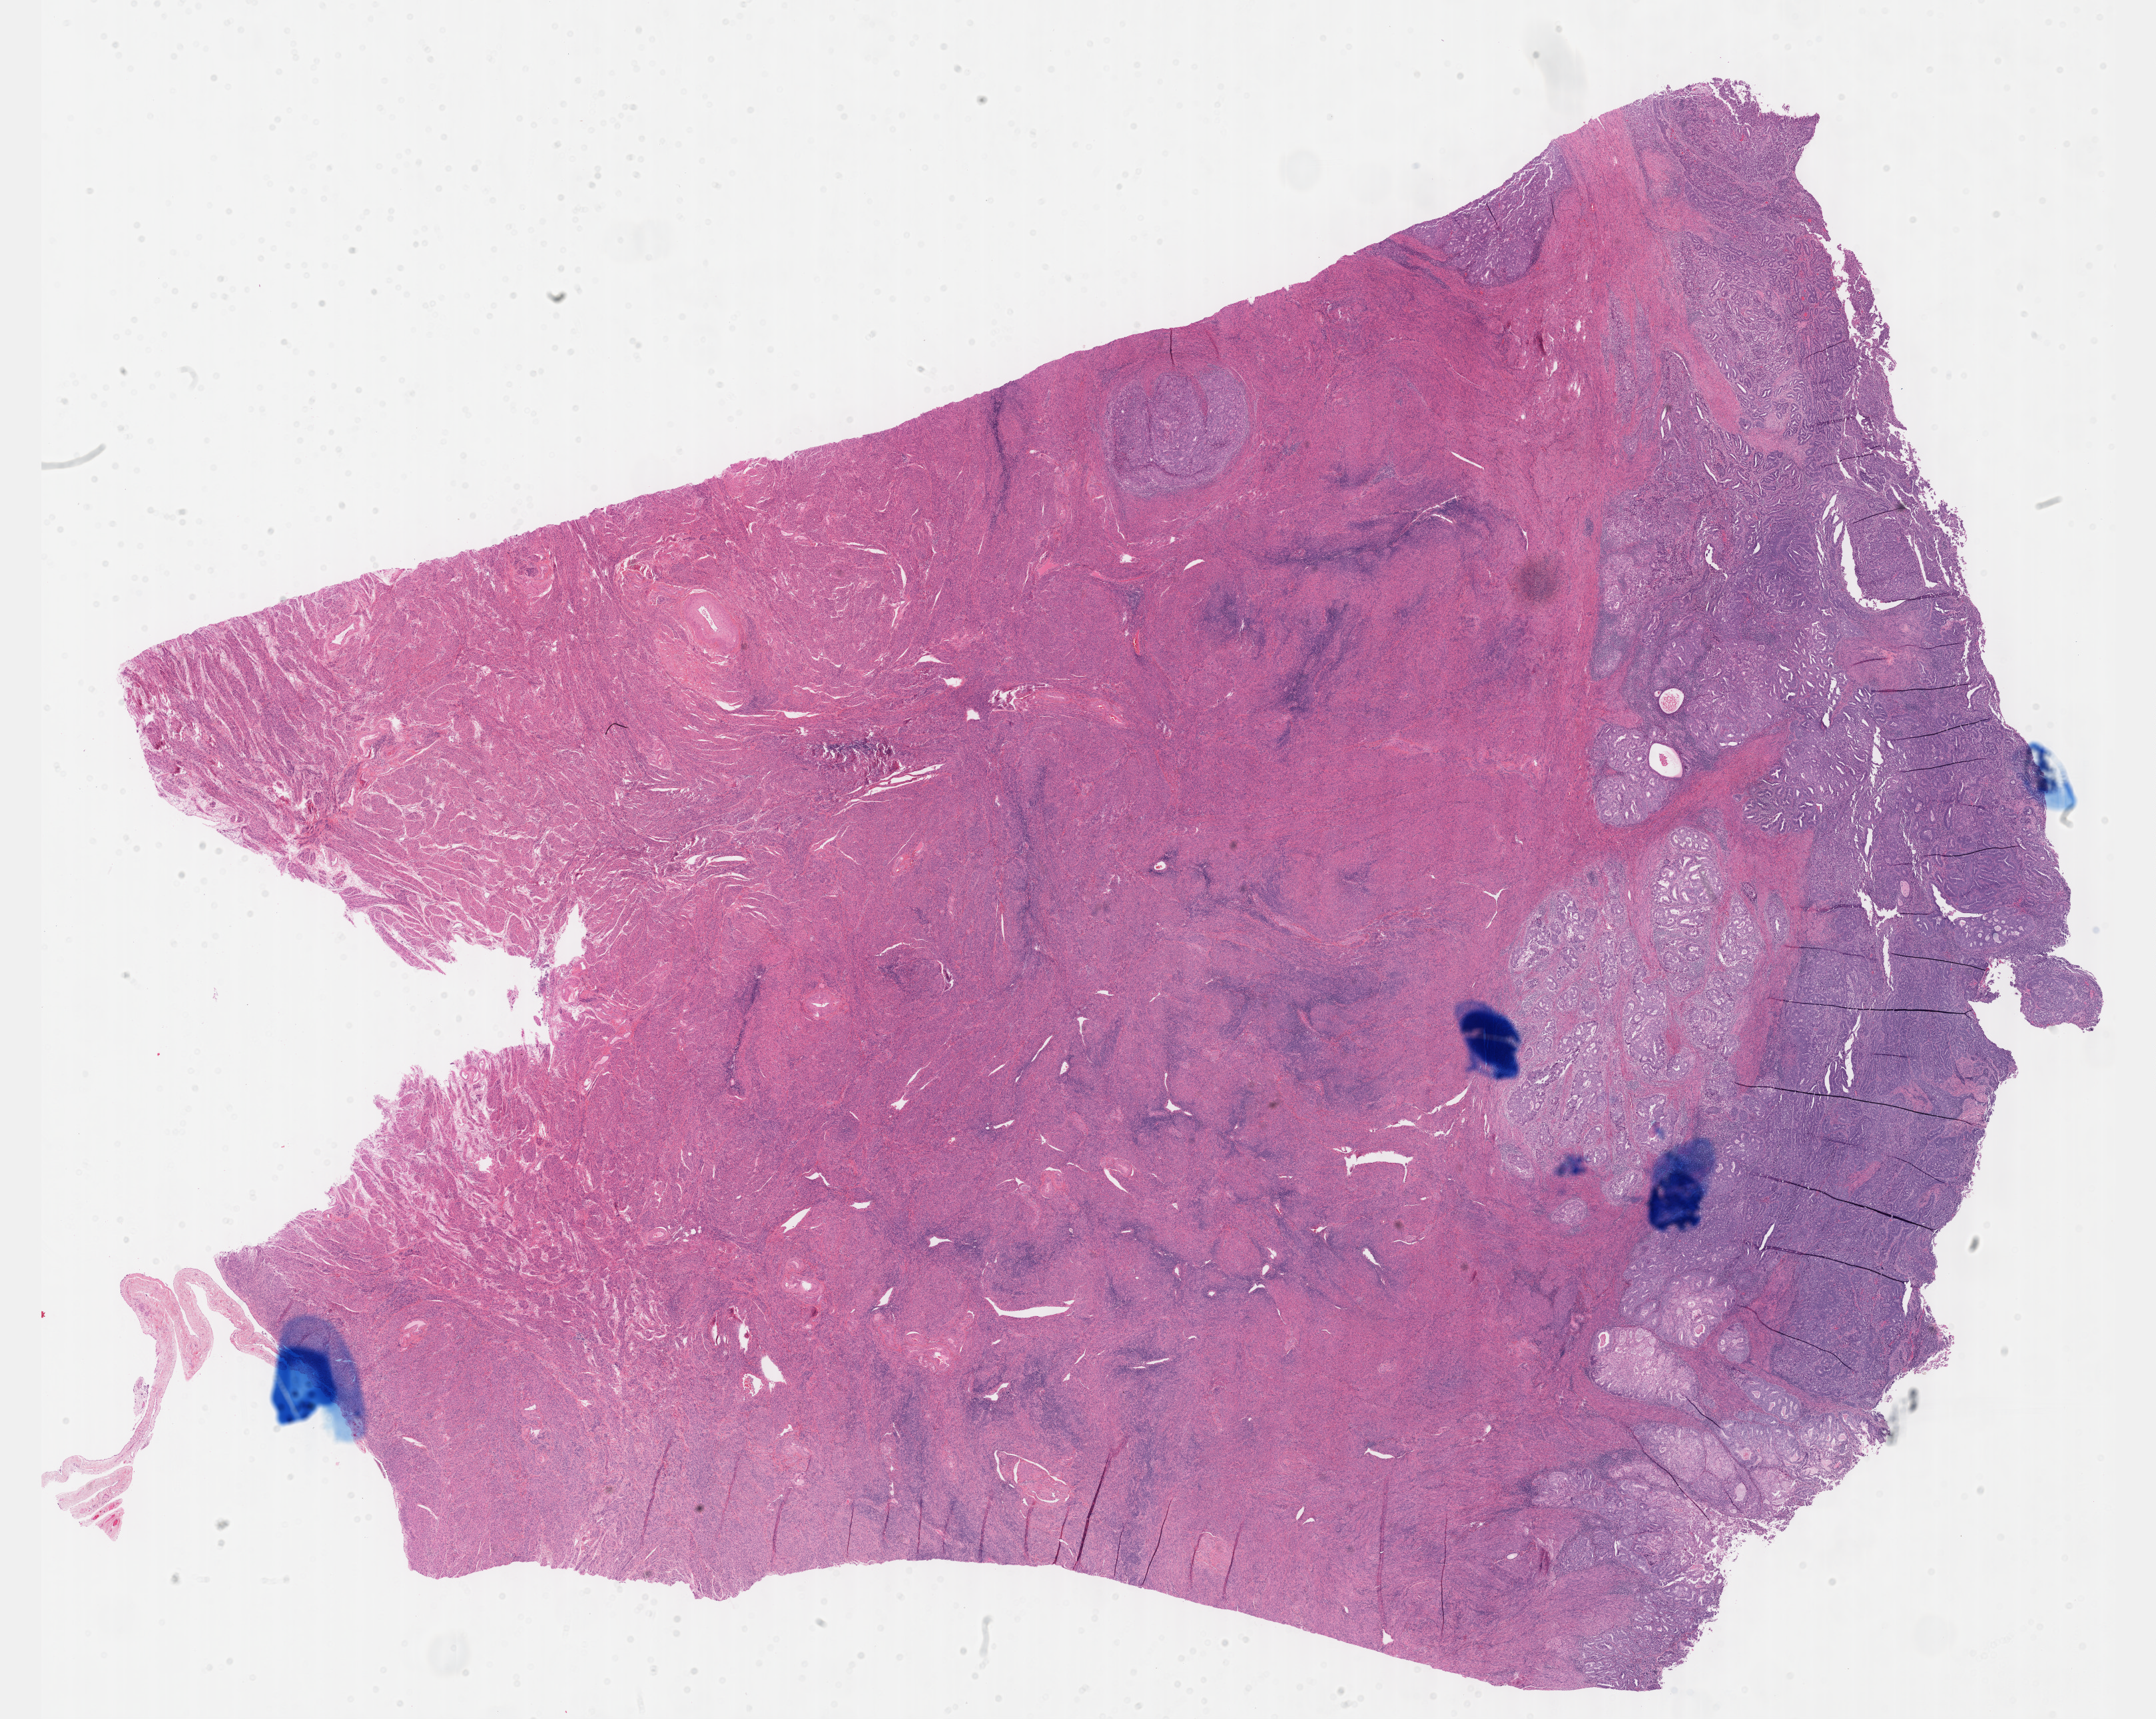
Whole-slide histology image, H&E-stained, a low-resolution overview of the entire scanned area, about 26.2 x 20.9 mm, FFPE section, uterus, primary tumour sample. Patient: female, age at initial diagnosis 74 years. Histologic grade: G2 (moderately differentiated).
Pathologic diagnosis: Endometrioid adenocarcinoma, NOS (endometrium). FIGO stage: IA.